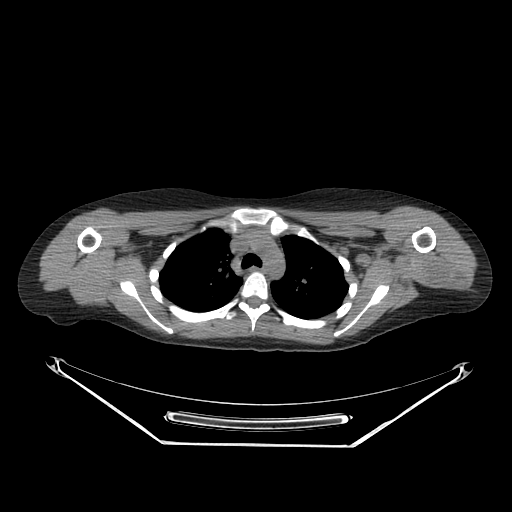
CT of an extremity soft-tissue mass (from a PET/CT study), one axial slice; position 205 of 267 along the scan axis; soft-tissue window (W 400 / L 40 HU); 512 × 512 image matrix, field of view 500 × 500 mm. Female patient. Case-level facts recorded for this patient, not image findings: histological type: malignant fibrous histiocytoma; grade: low; site of the primary tumour: left arm.
Structures marked on this image (expert contour drawn on MRI and transferred to this co-registered scan by the dataset authors):
- gross tumour volume (mass): bounding box (x1, y1, x2, y2) in pixels: (422, 249, 458, 284)